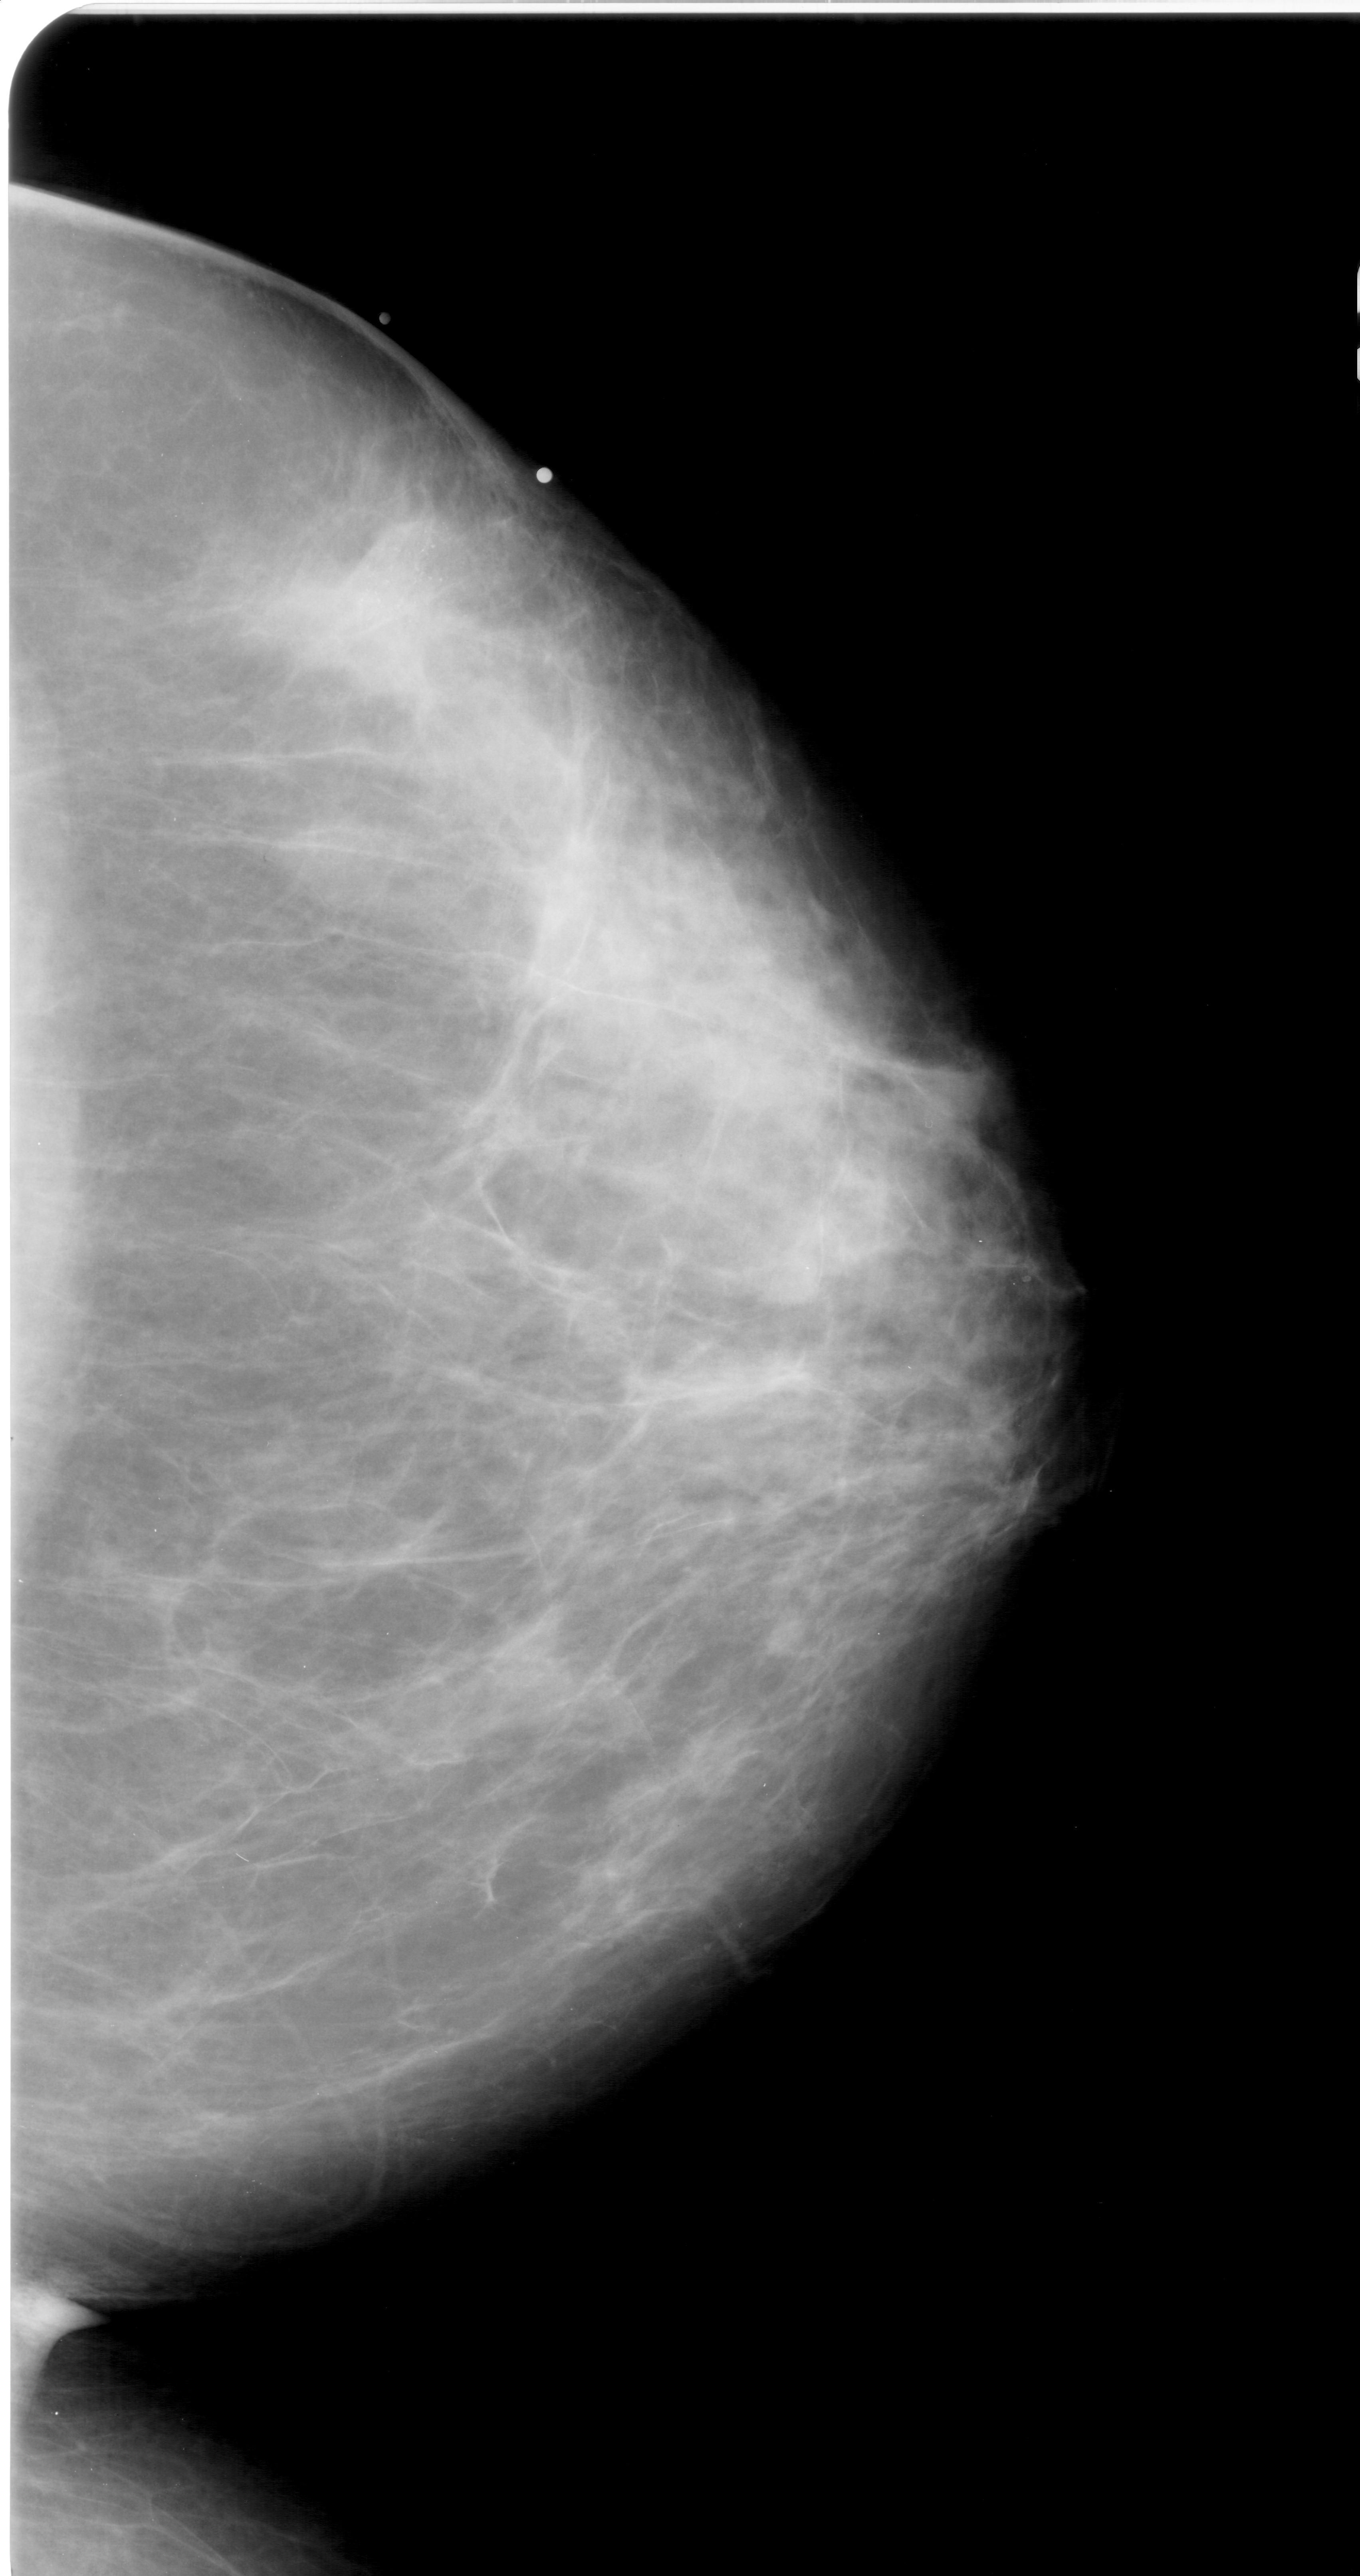
Digitized screen-film mammogram. Right breast. Craniocaudal (CC) view. BI-RADS breast density category 3 (scale 1–4). 1360 × 2576 image matrix.
Expert-marked regions of interest on this film, with their recorded descriptors:
- calcifications, morphology pleomorphic, distribution clustered; BI-RADS assessment category 4; pathology result (as recorded, not read from the image): malignant: bounding box (x1, y1, x2, y2) in pixels: (368, 538, 469, 712)